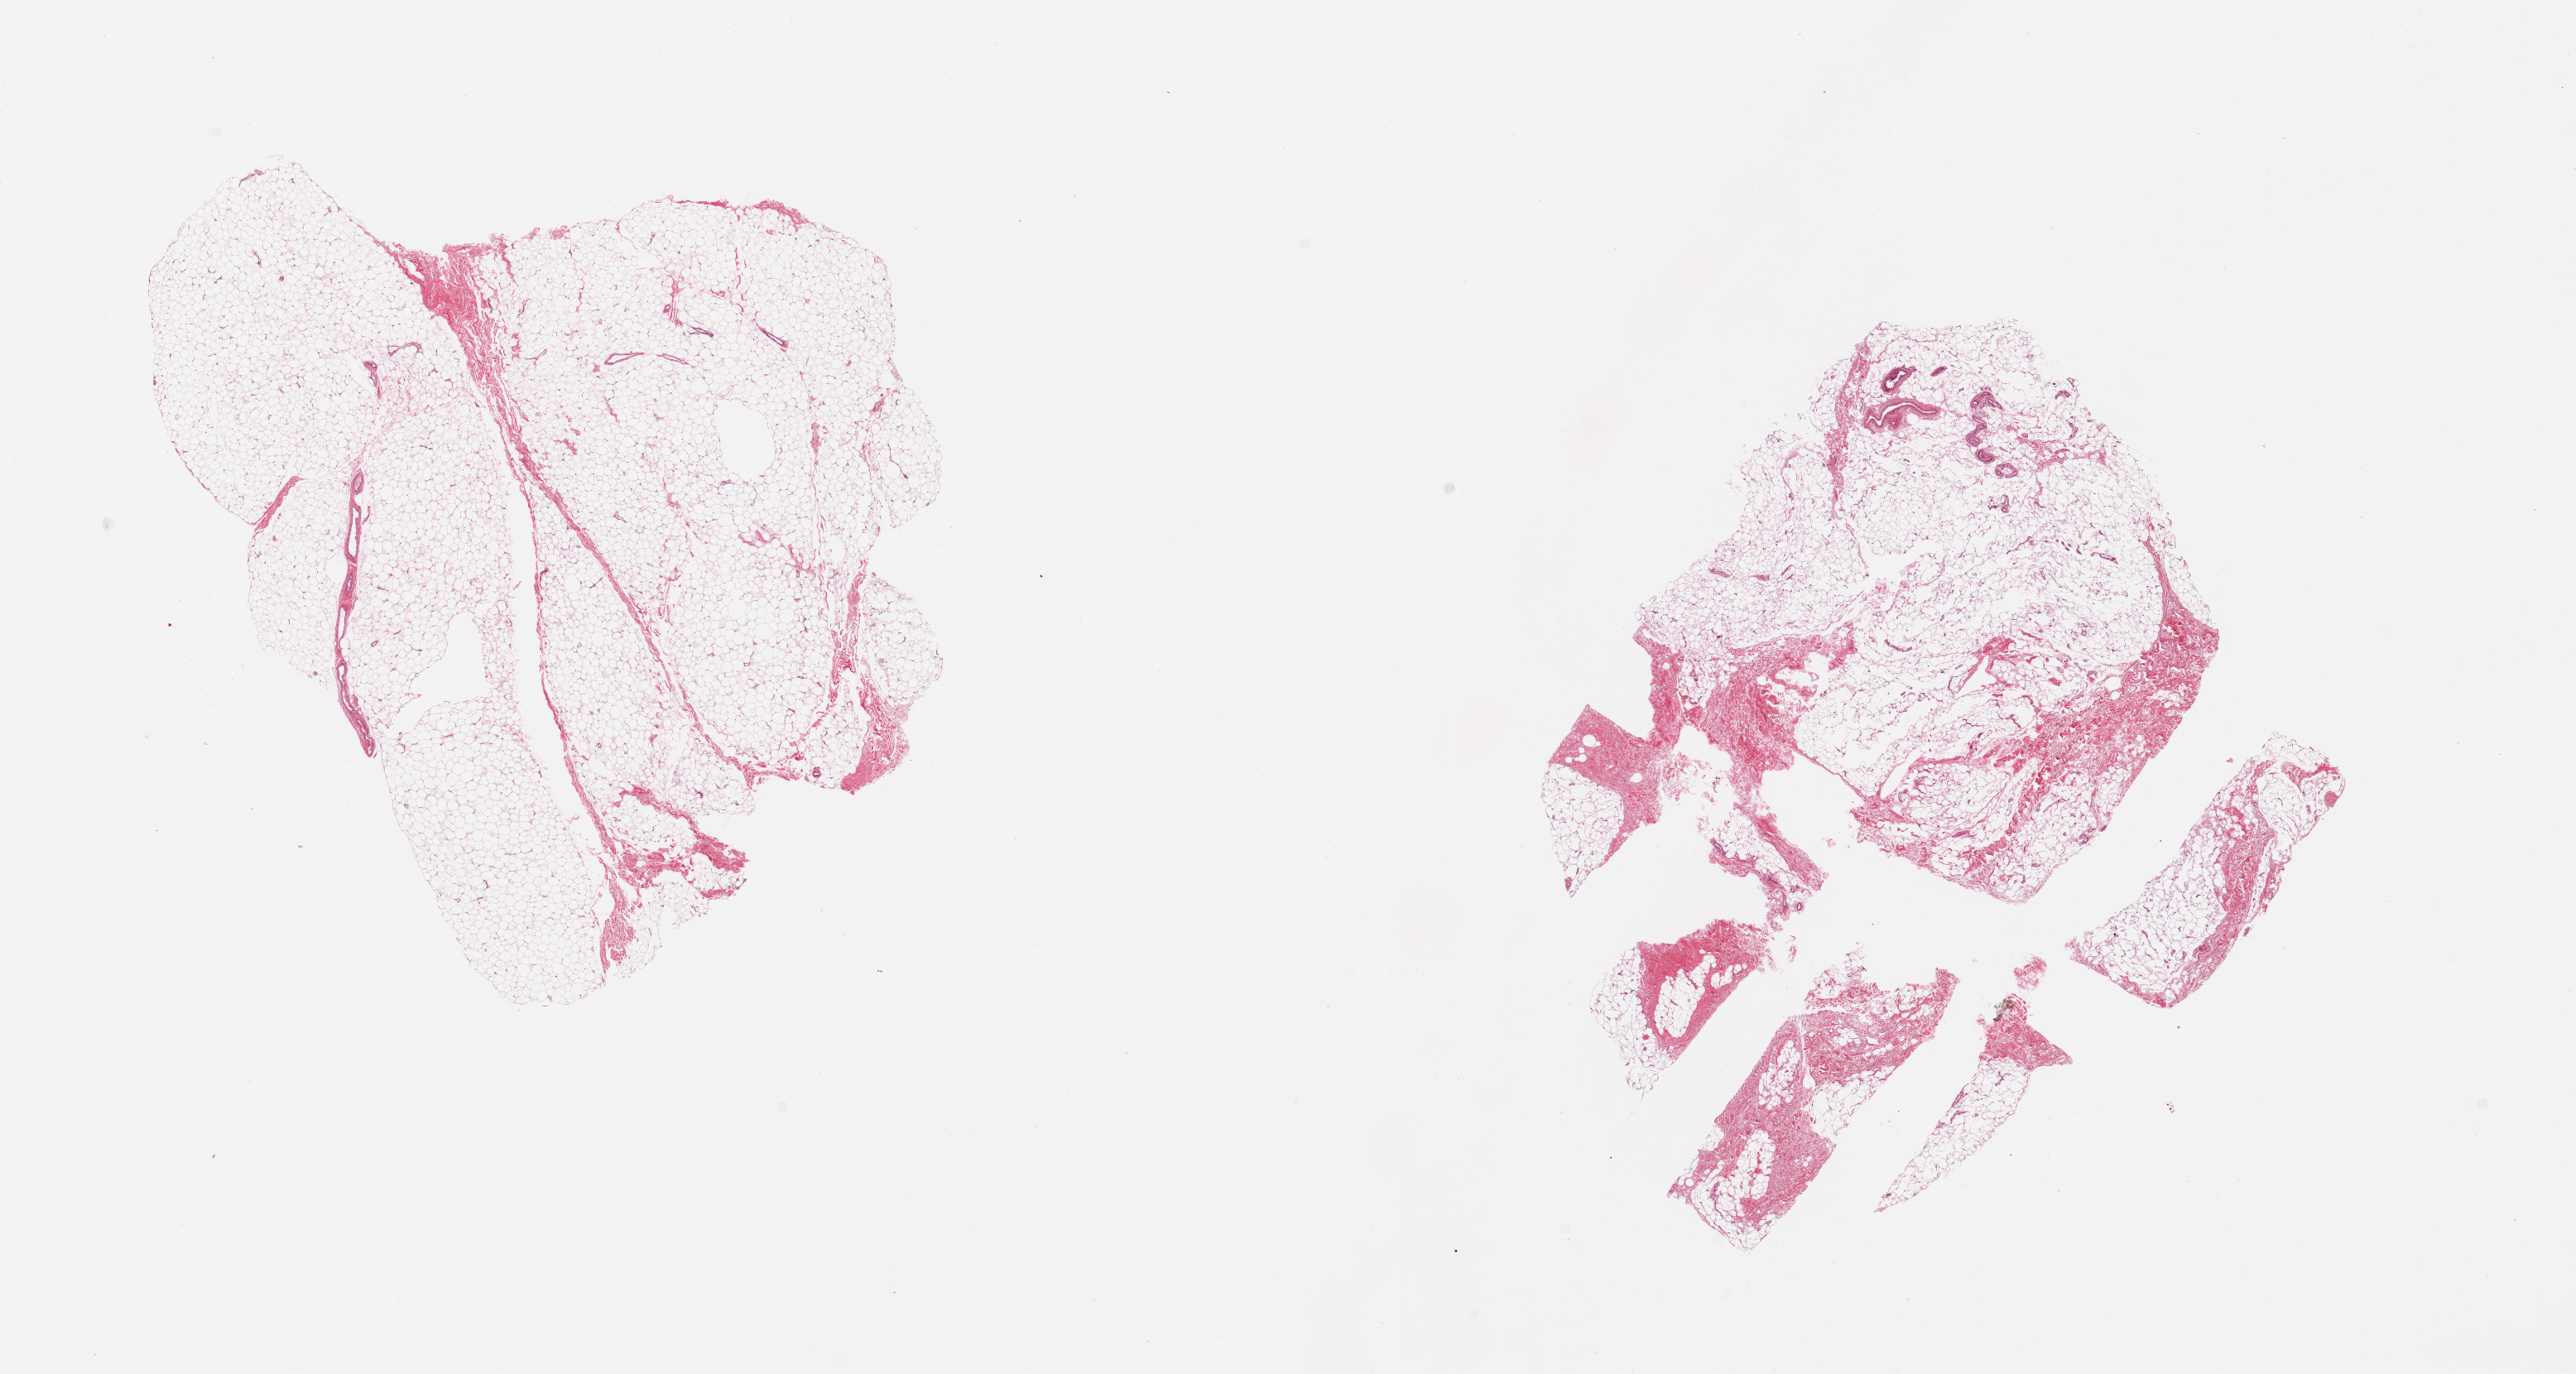
Digitized hematoxylin and eosin (H&E)-stained section, shown as a low-resolution overview of the whole scanned area (about 24.6 x 13.1 mm, acquisition: 20x scan). PAXgene-fixed paraffin-embedded (PFPE) section. Target tissue: breast. Tissue donor sample. Male donor.
- pathologist's review note for this sample: 2 pieces; fibroadipose tissue, no ductal elements